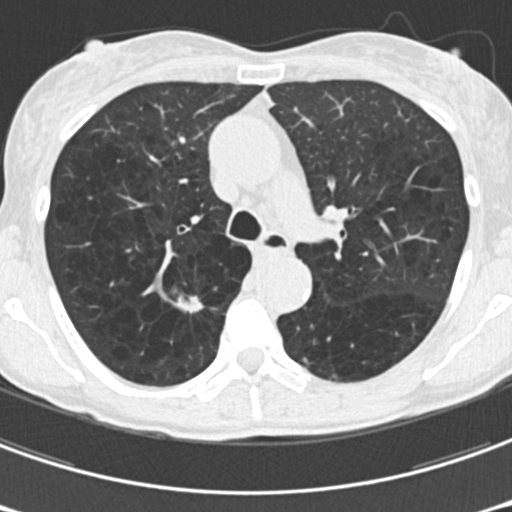
Axial slice from a low-dose chest CT screening exam. Third screening round (two years after baseline). Lung window (W 1500 / L -600 HU). Standard (soft-tissue) reconstruction kernel (B30f). 120 kVp. Slice 60 of 176 in the series. Female participant, aged 61 years at enrolment.
Expert reader's lesion annotation, bounding box <162,281,218,335> (left, top, right, bottom; pixels). The screening reader recorded 2 non-calcified nodules or masses ≥4 mm on this exam (right upper lobe, right upper lobe); which of them this box marks is not recorded. Official screen result: positive, other. Later outcome: lung cancer diagnosed 77 days after this screen — non-small cell carcinoma, right upper lobe, undifferentiated (G4), stage IA (AJCC 6th edition), 15 mm at pathology.